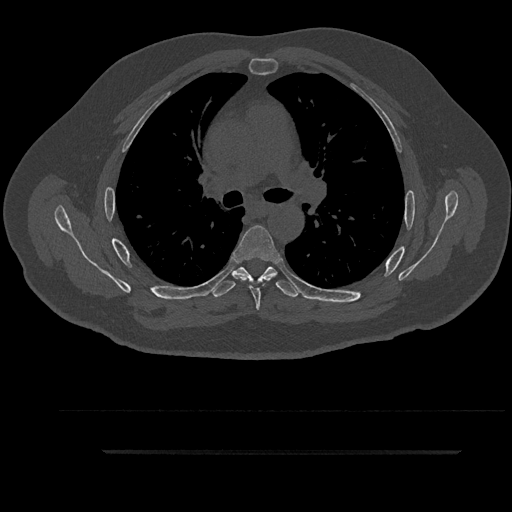
CT including the spine, one axial slice; slice 608 of 797 in the series (ordered by position); 120 kVp; bone window (W 1800 / L 400 HU); 0.5 mm slice thickness; 512 × 512 image matrix, field of view 432 × 432 mm. Patient: male, 63 years. From the clinical record (not read from this slice): primary cancer: renal.
Structures marked on this image (semi-automatic segmentation, software-assisted and operator-edited):
- T5 vertebra: bounding box <233,225,282,310> (left, top, right, bottom; pixels)
- T6 vertebra: <212,266,299,298>